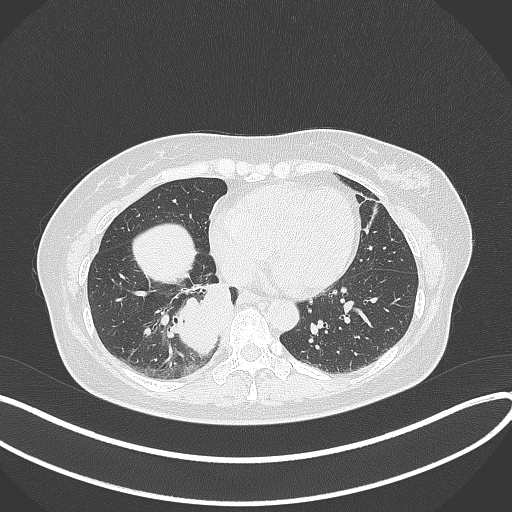
Chest CT, one axial slice; slice 121 of 331 in the series (ordered by position); 120 kVp; lung window (W 1500 / L -600 HU); 1 mm slice thickness; 512 × 512 image matrix, field of view 400 × 400 mm. Patient: female, 54 years. Case-level facts recorded for this patient, not image findings: clinical TNM (as recorded): T4 N0 M0.
Annotated regions visible in this slice (bounding box drawn by a radiologist):
- lung tumour (recorded histology: adenocarcinoma): bounding box (x1, y1, x2, y2) in pixels: (165, 275, 235, 355)